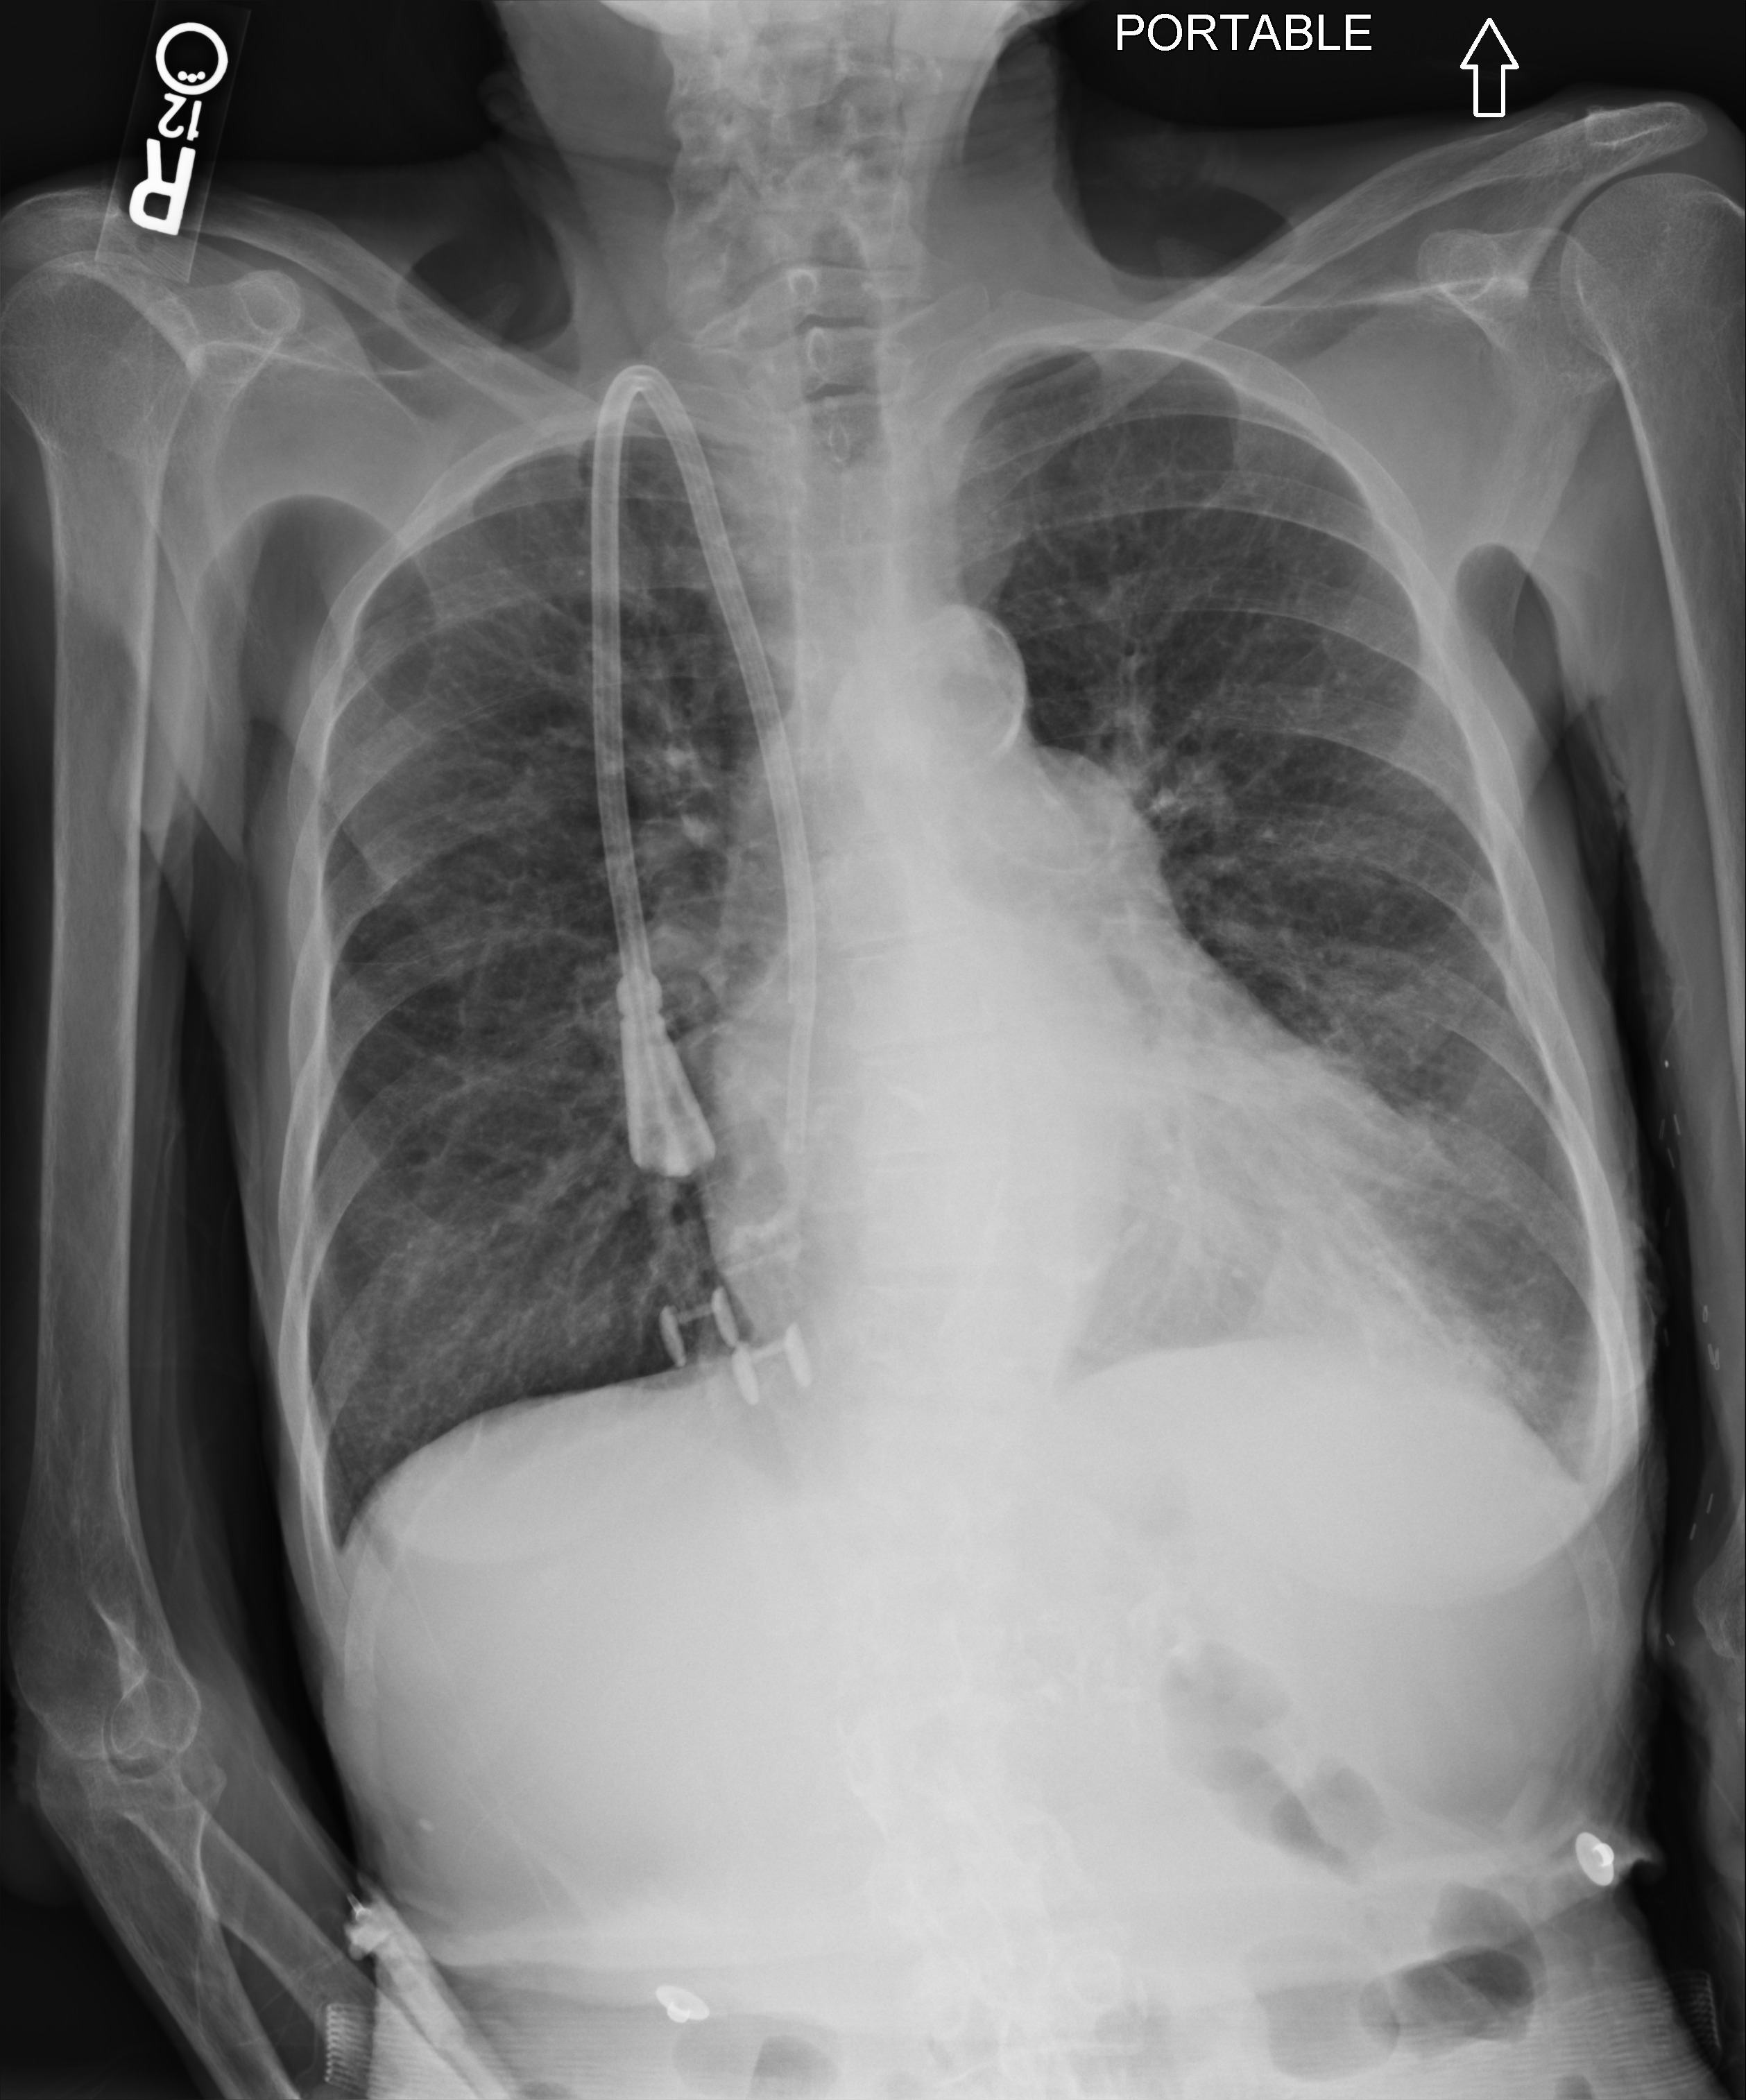
Portable chest radiograph, anteroposterior (AP) projection. Female patient hospitalised with COVID-19, age 60–74 years.
Hospital-stay facts (about this admission, not read from this image; timing relative to this image not recorded):
- admitted to intensive care during this hospital stay: no